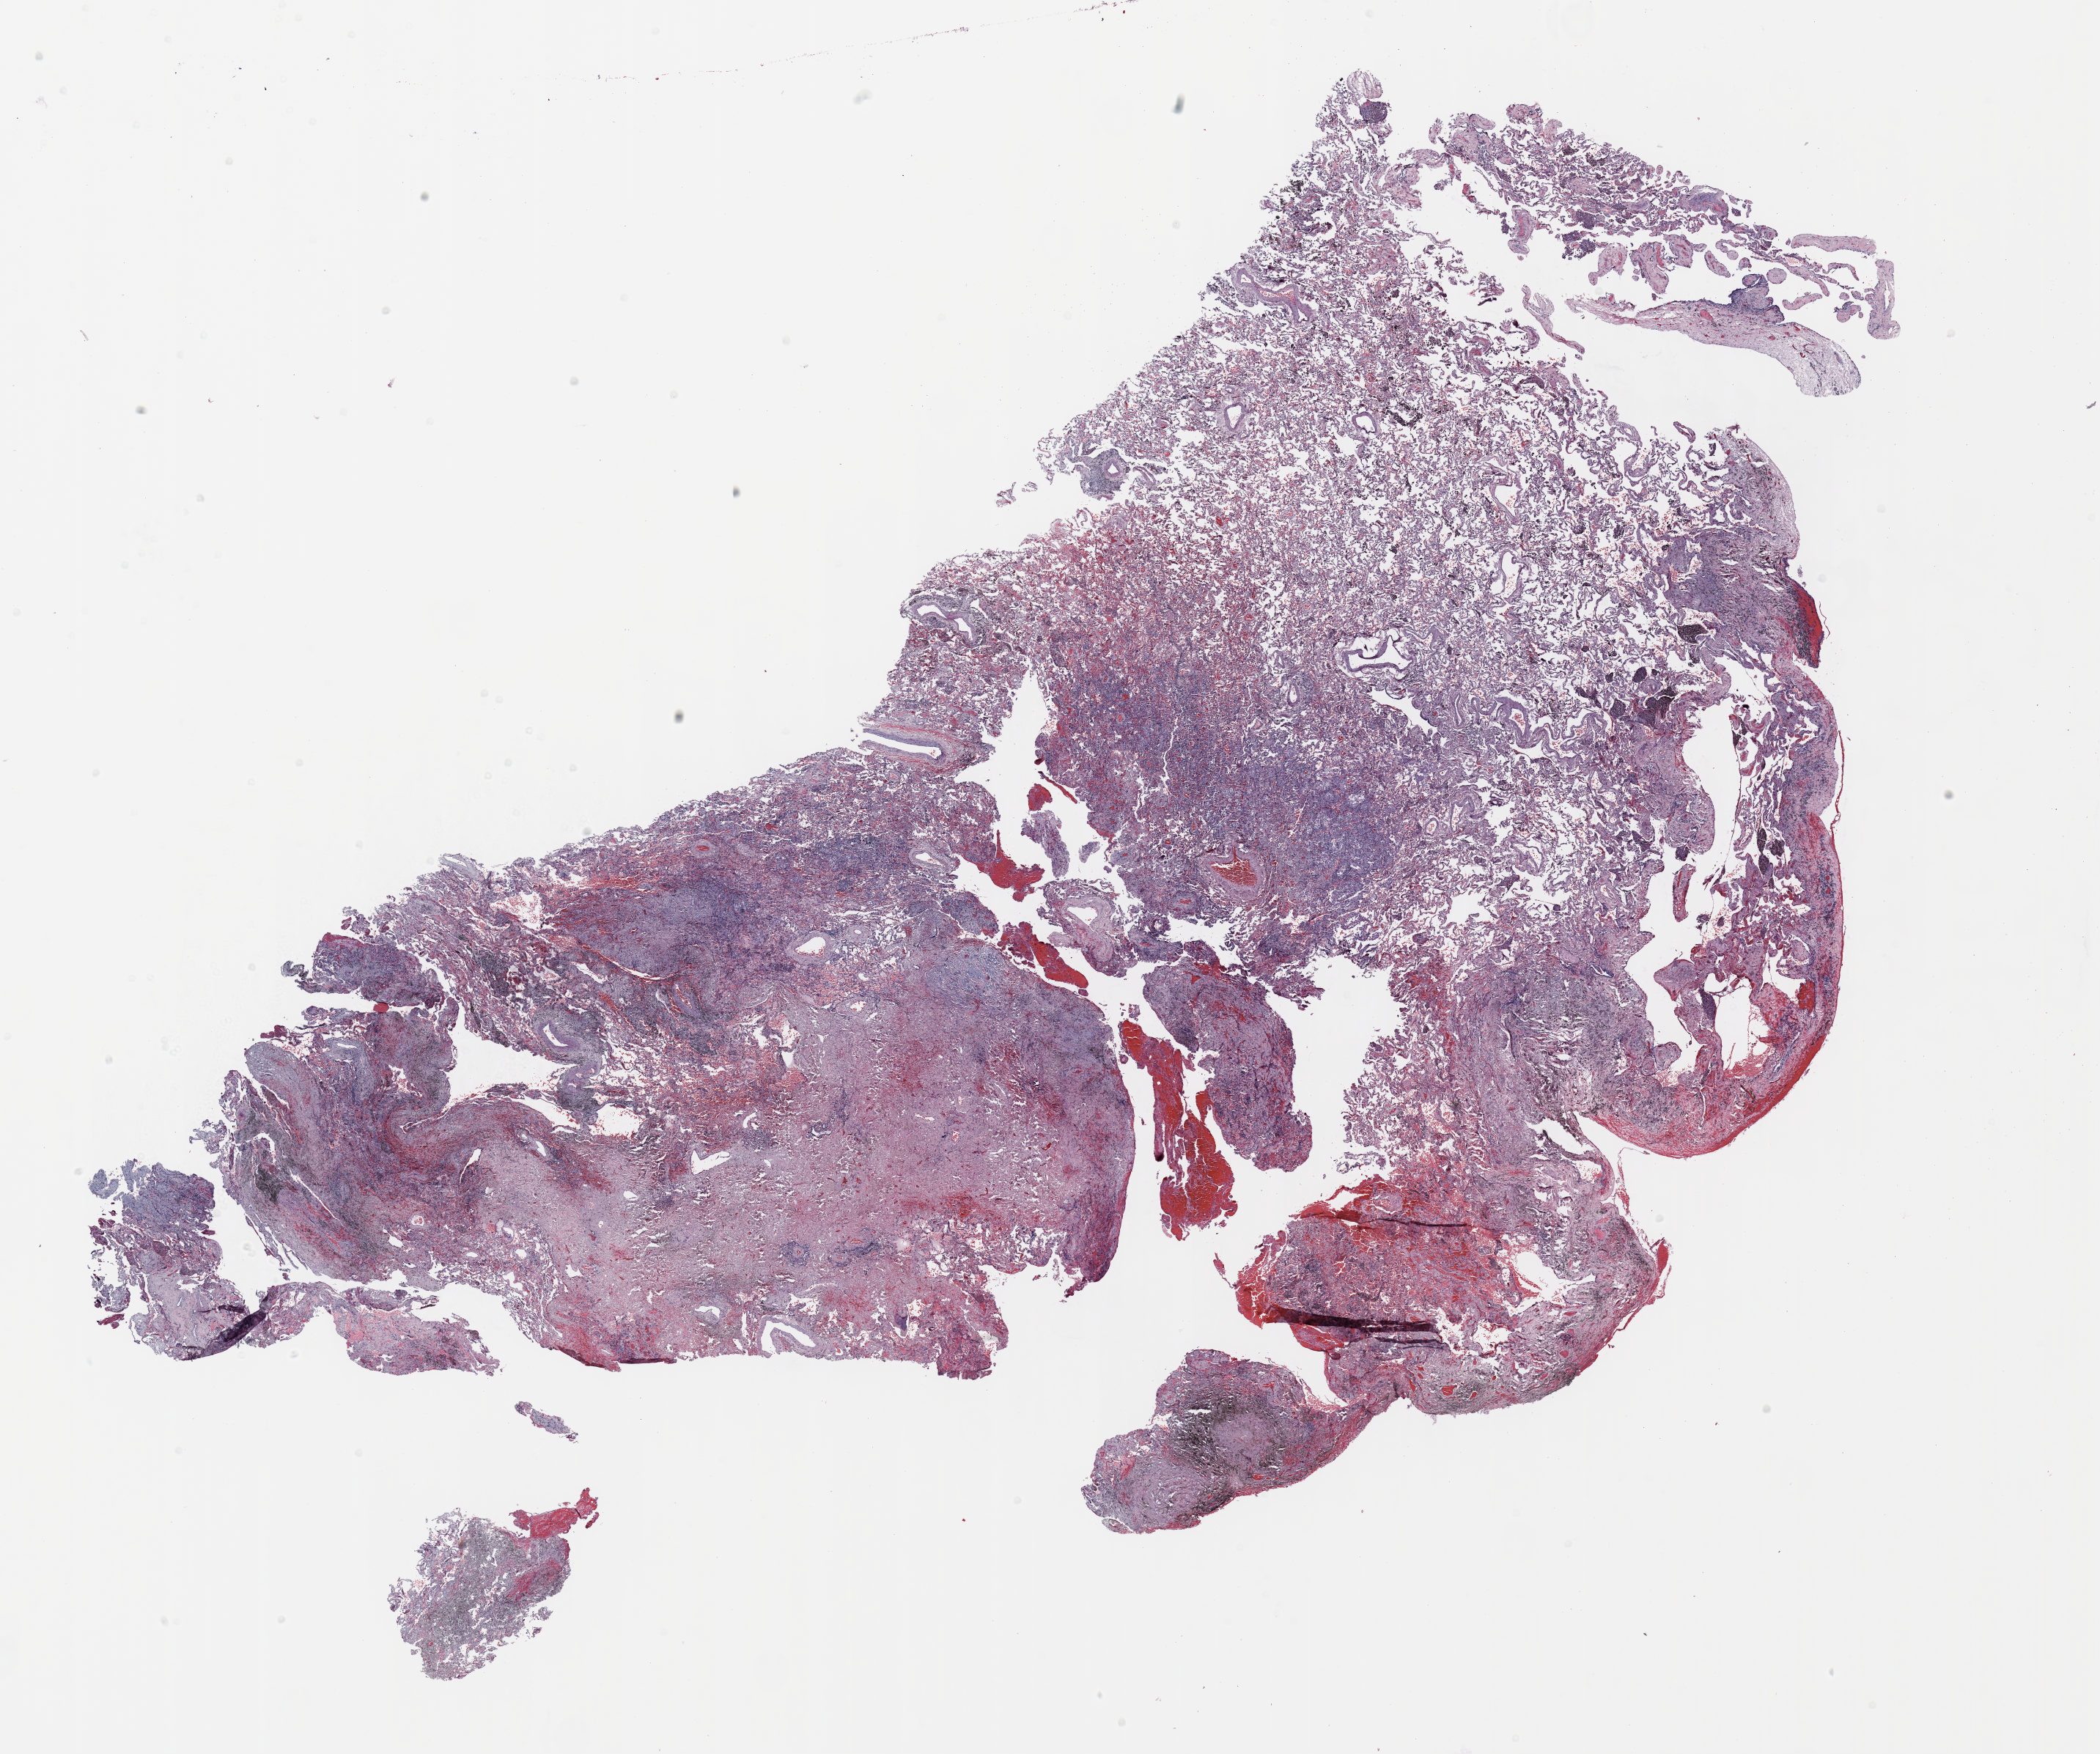
Whole-slide histology image, H&E — whole scanned area (about 23.0 x 19.2 mm) shown as a low-resolution overview. FFPE section. Lung tissue. Male patient, aged 63 at enrolment. Current smoker at enrolment. Grade: moderately differentiated (G2).
Participant's lung-cancer diagnosis: Bronchiolo-alveolar adenocarcinoma, NOS. Stage (AJCC 6th edition): IA. Tumour size (pathology): 15 mm. Primary tumour location (clinical record): right upper lobe.